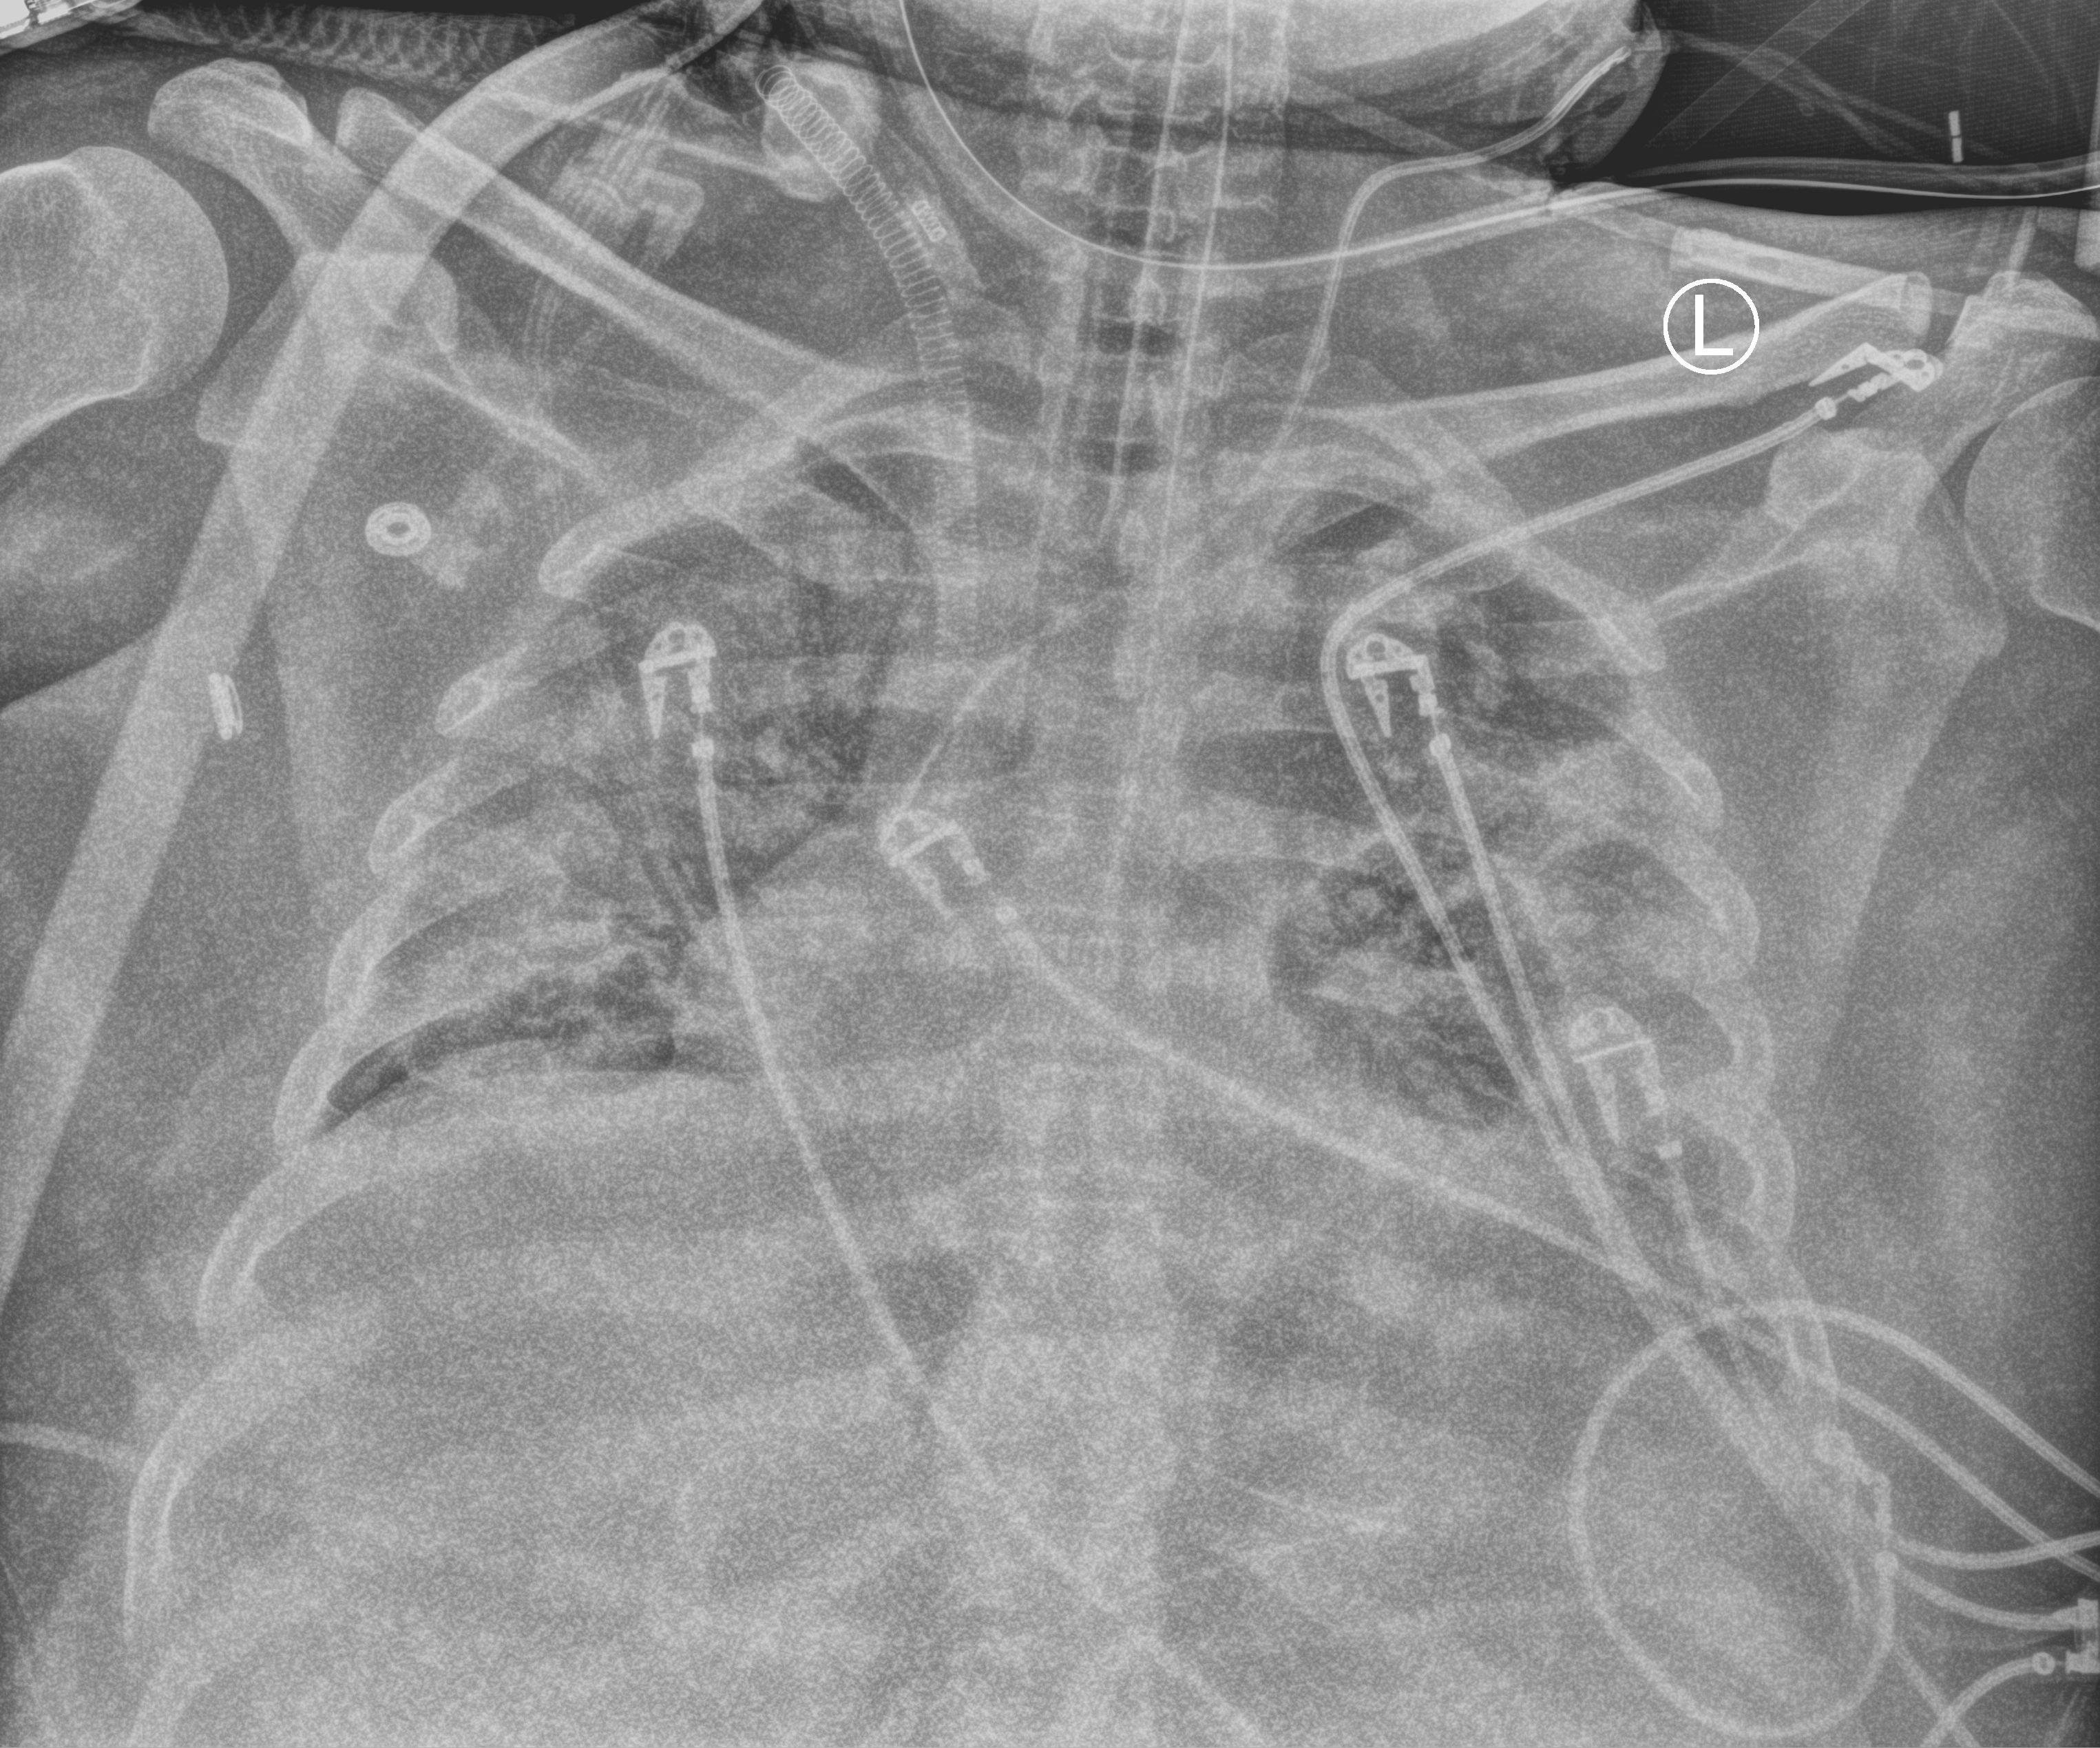
Portable chest radiograph; anteroposterior (AP) projection. Adult patient hospitalised with COVID-19, age 18–59 years.
Hospital-stay facts (about this admission, not read from this image; timing relative to this image not recorded): admitted to intensive care during this hospital stay: yes; mechanically ventilated during this hospital stay: yes; smoking status (admission record): never.